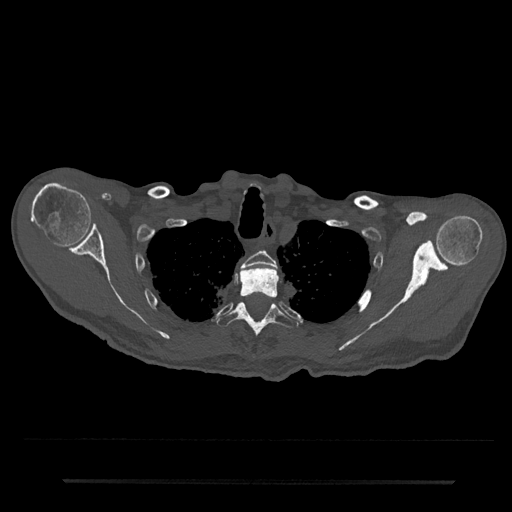
CT including the spine, one axial slice; slice 646 of 797 in the series (ordered by position); reconstruction kernel Br40s/3; bone window (W 1800 / L 400 HU); 0.5 mm slice thickness; 512 × 512 image matrix, field of view 427 × 427 mm. Patient: male, 74 years. From the clinical record (not read from this slice): primary cancer: prostate.
Annotated regions visible in this slice (semi-automatically segmented with operator editing):
- T2 vertebra: bounding box <241,250,277,269> (left, top, right, bottom; pixels)
- T3 vertebra: <239,266,278,299>
- T4 vertebra: <216,302,299,338>